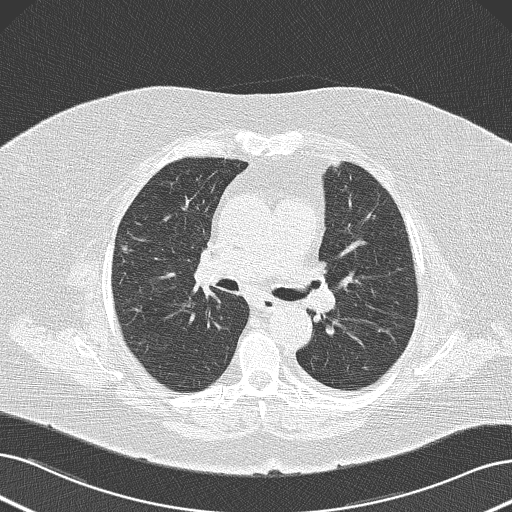
Low-dose screening chest CT, one axial slice; position 81 of 145 along the scan axis; lung window (W 1500 / L -600 HU); 2 mm slice thickness; 512 × 512 image matrix, field of view 364 × 364 mm.
Outlined on this slice (outlined manually by an expert reader):
- lesion 1 (tumor, upper lobe of right lung): bounding box <121,242,132,253> (left, top, right, bottom; pixels)